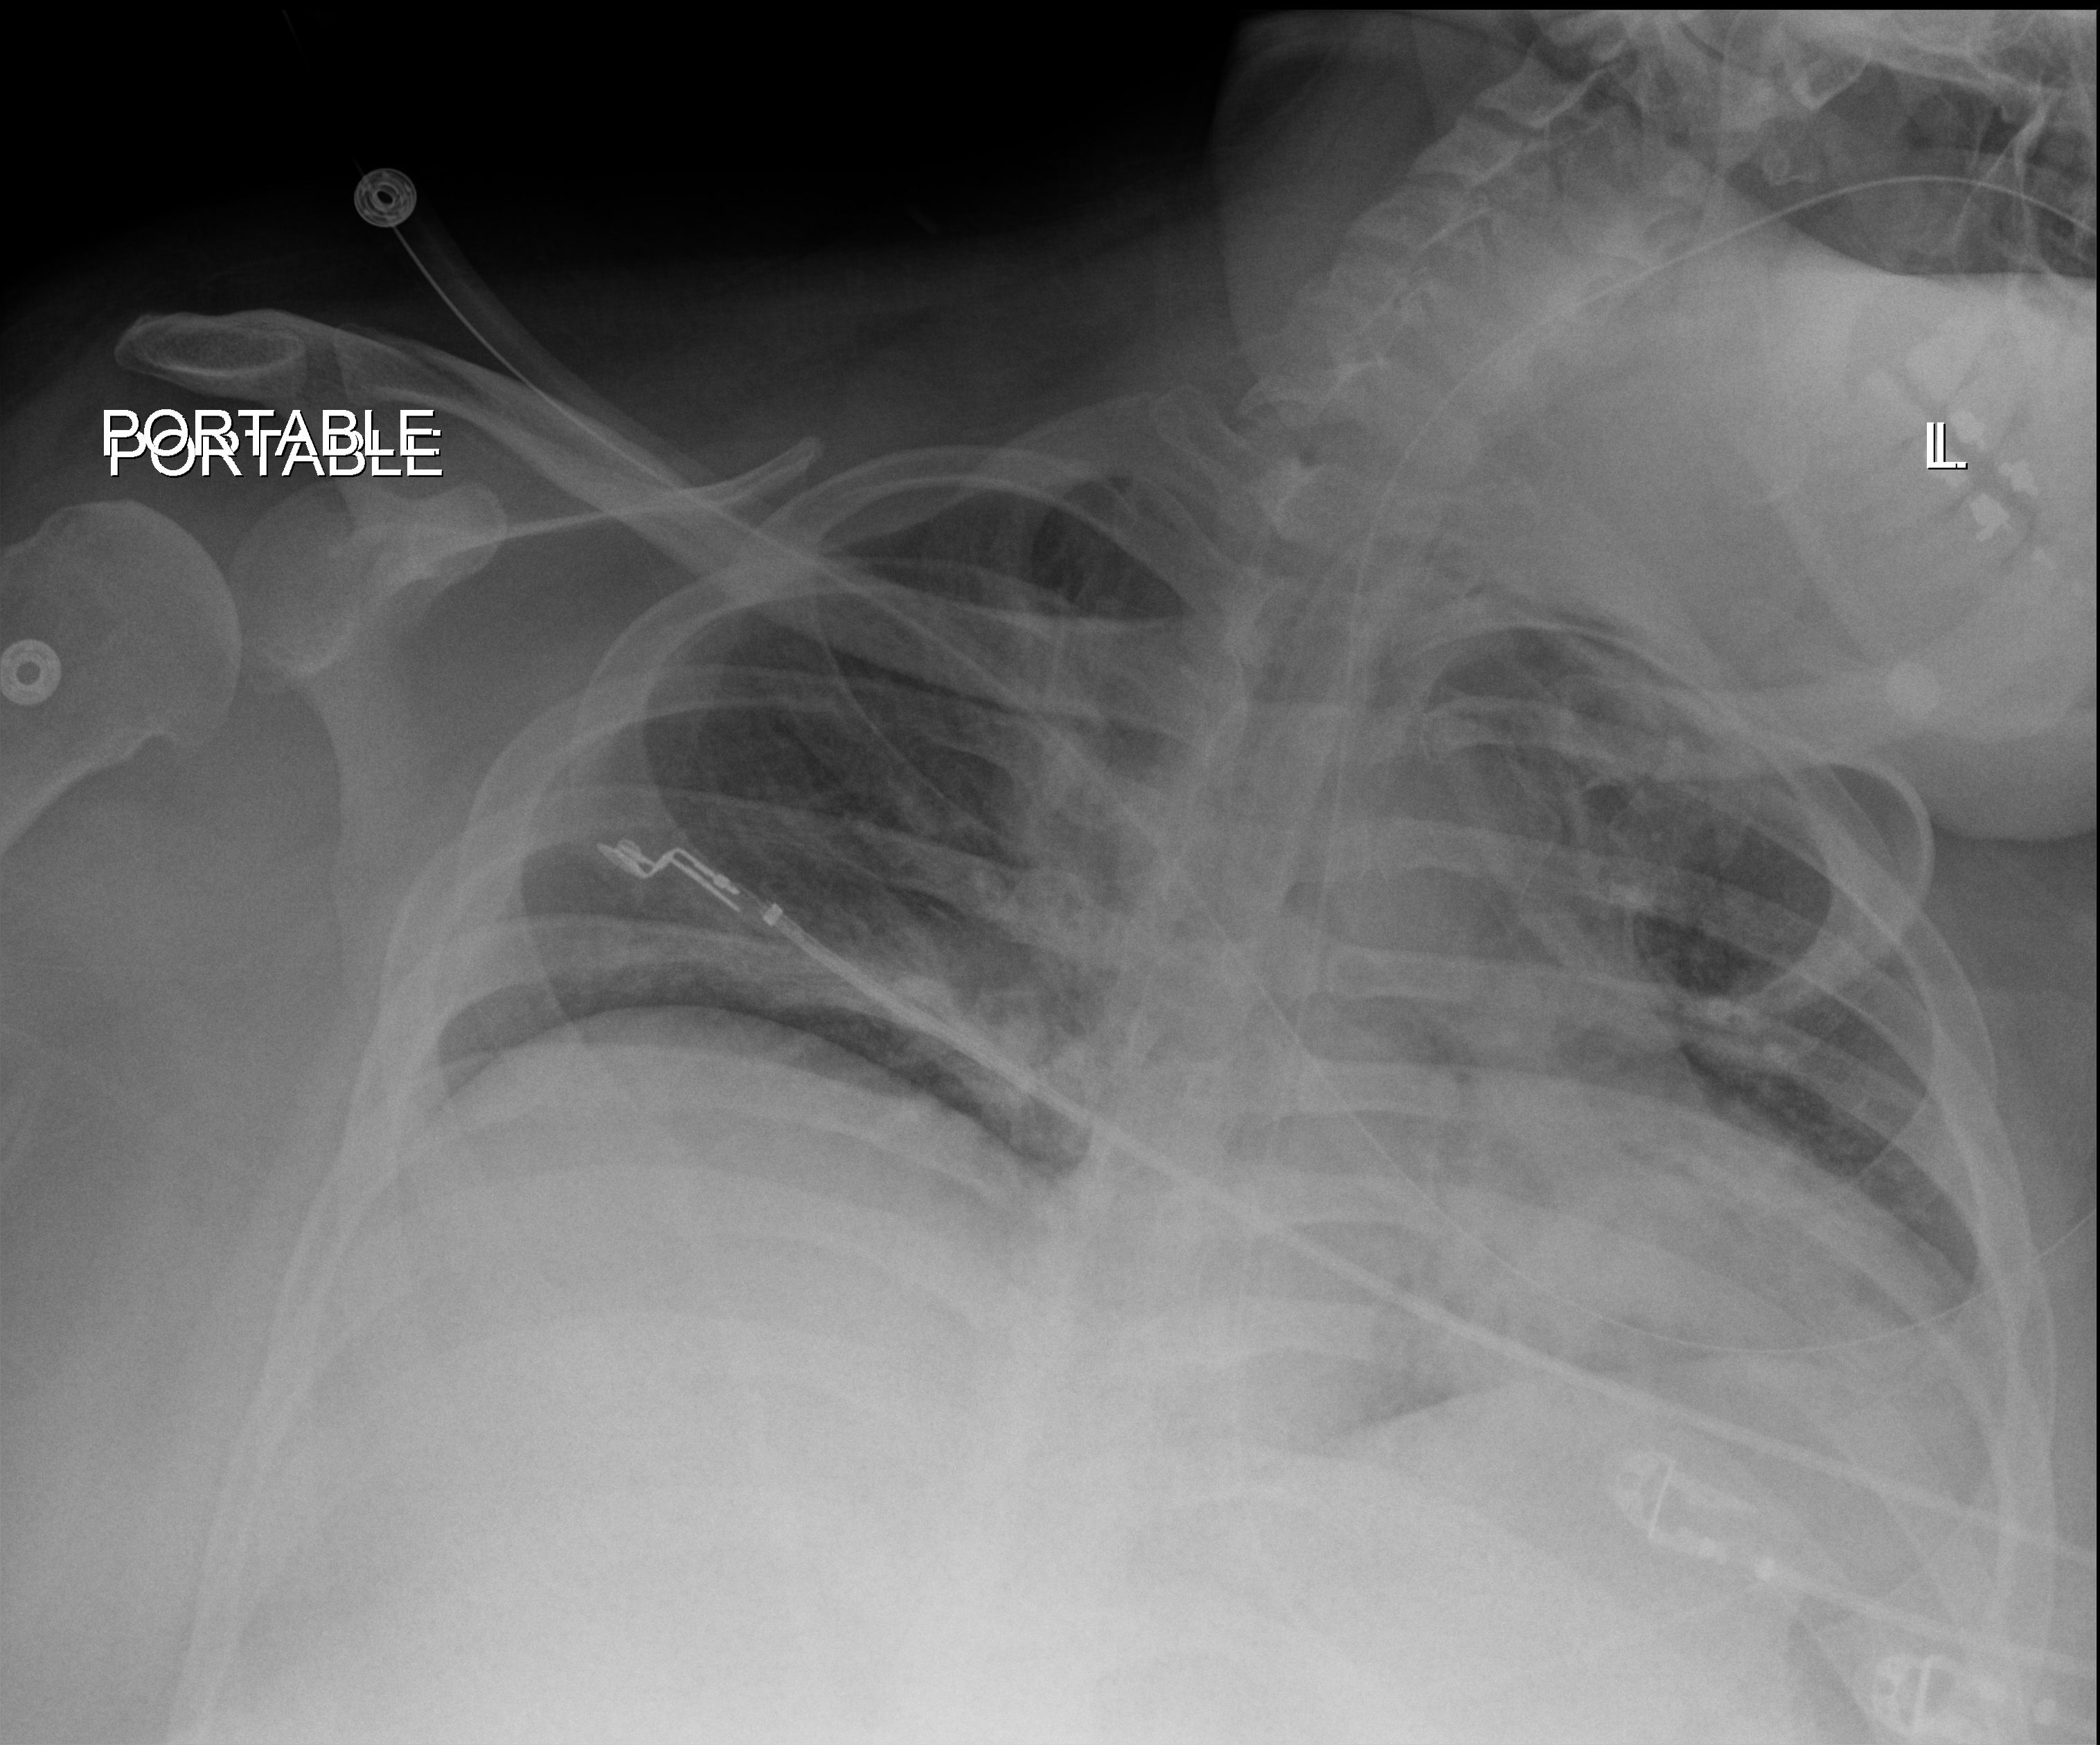
Chest X-ray (portable); anteroposterior (AP) projection. Patient hospitalised with COVID-19; male, aged 18–59 years.
Hospital-stay facts (about this admission, not read from this image; timing relative to this image not recorded): admitted to intensive care during this hospital stay: yes; mechanically ventilated during this hospital stay: yes.